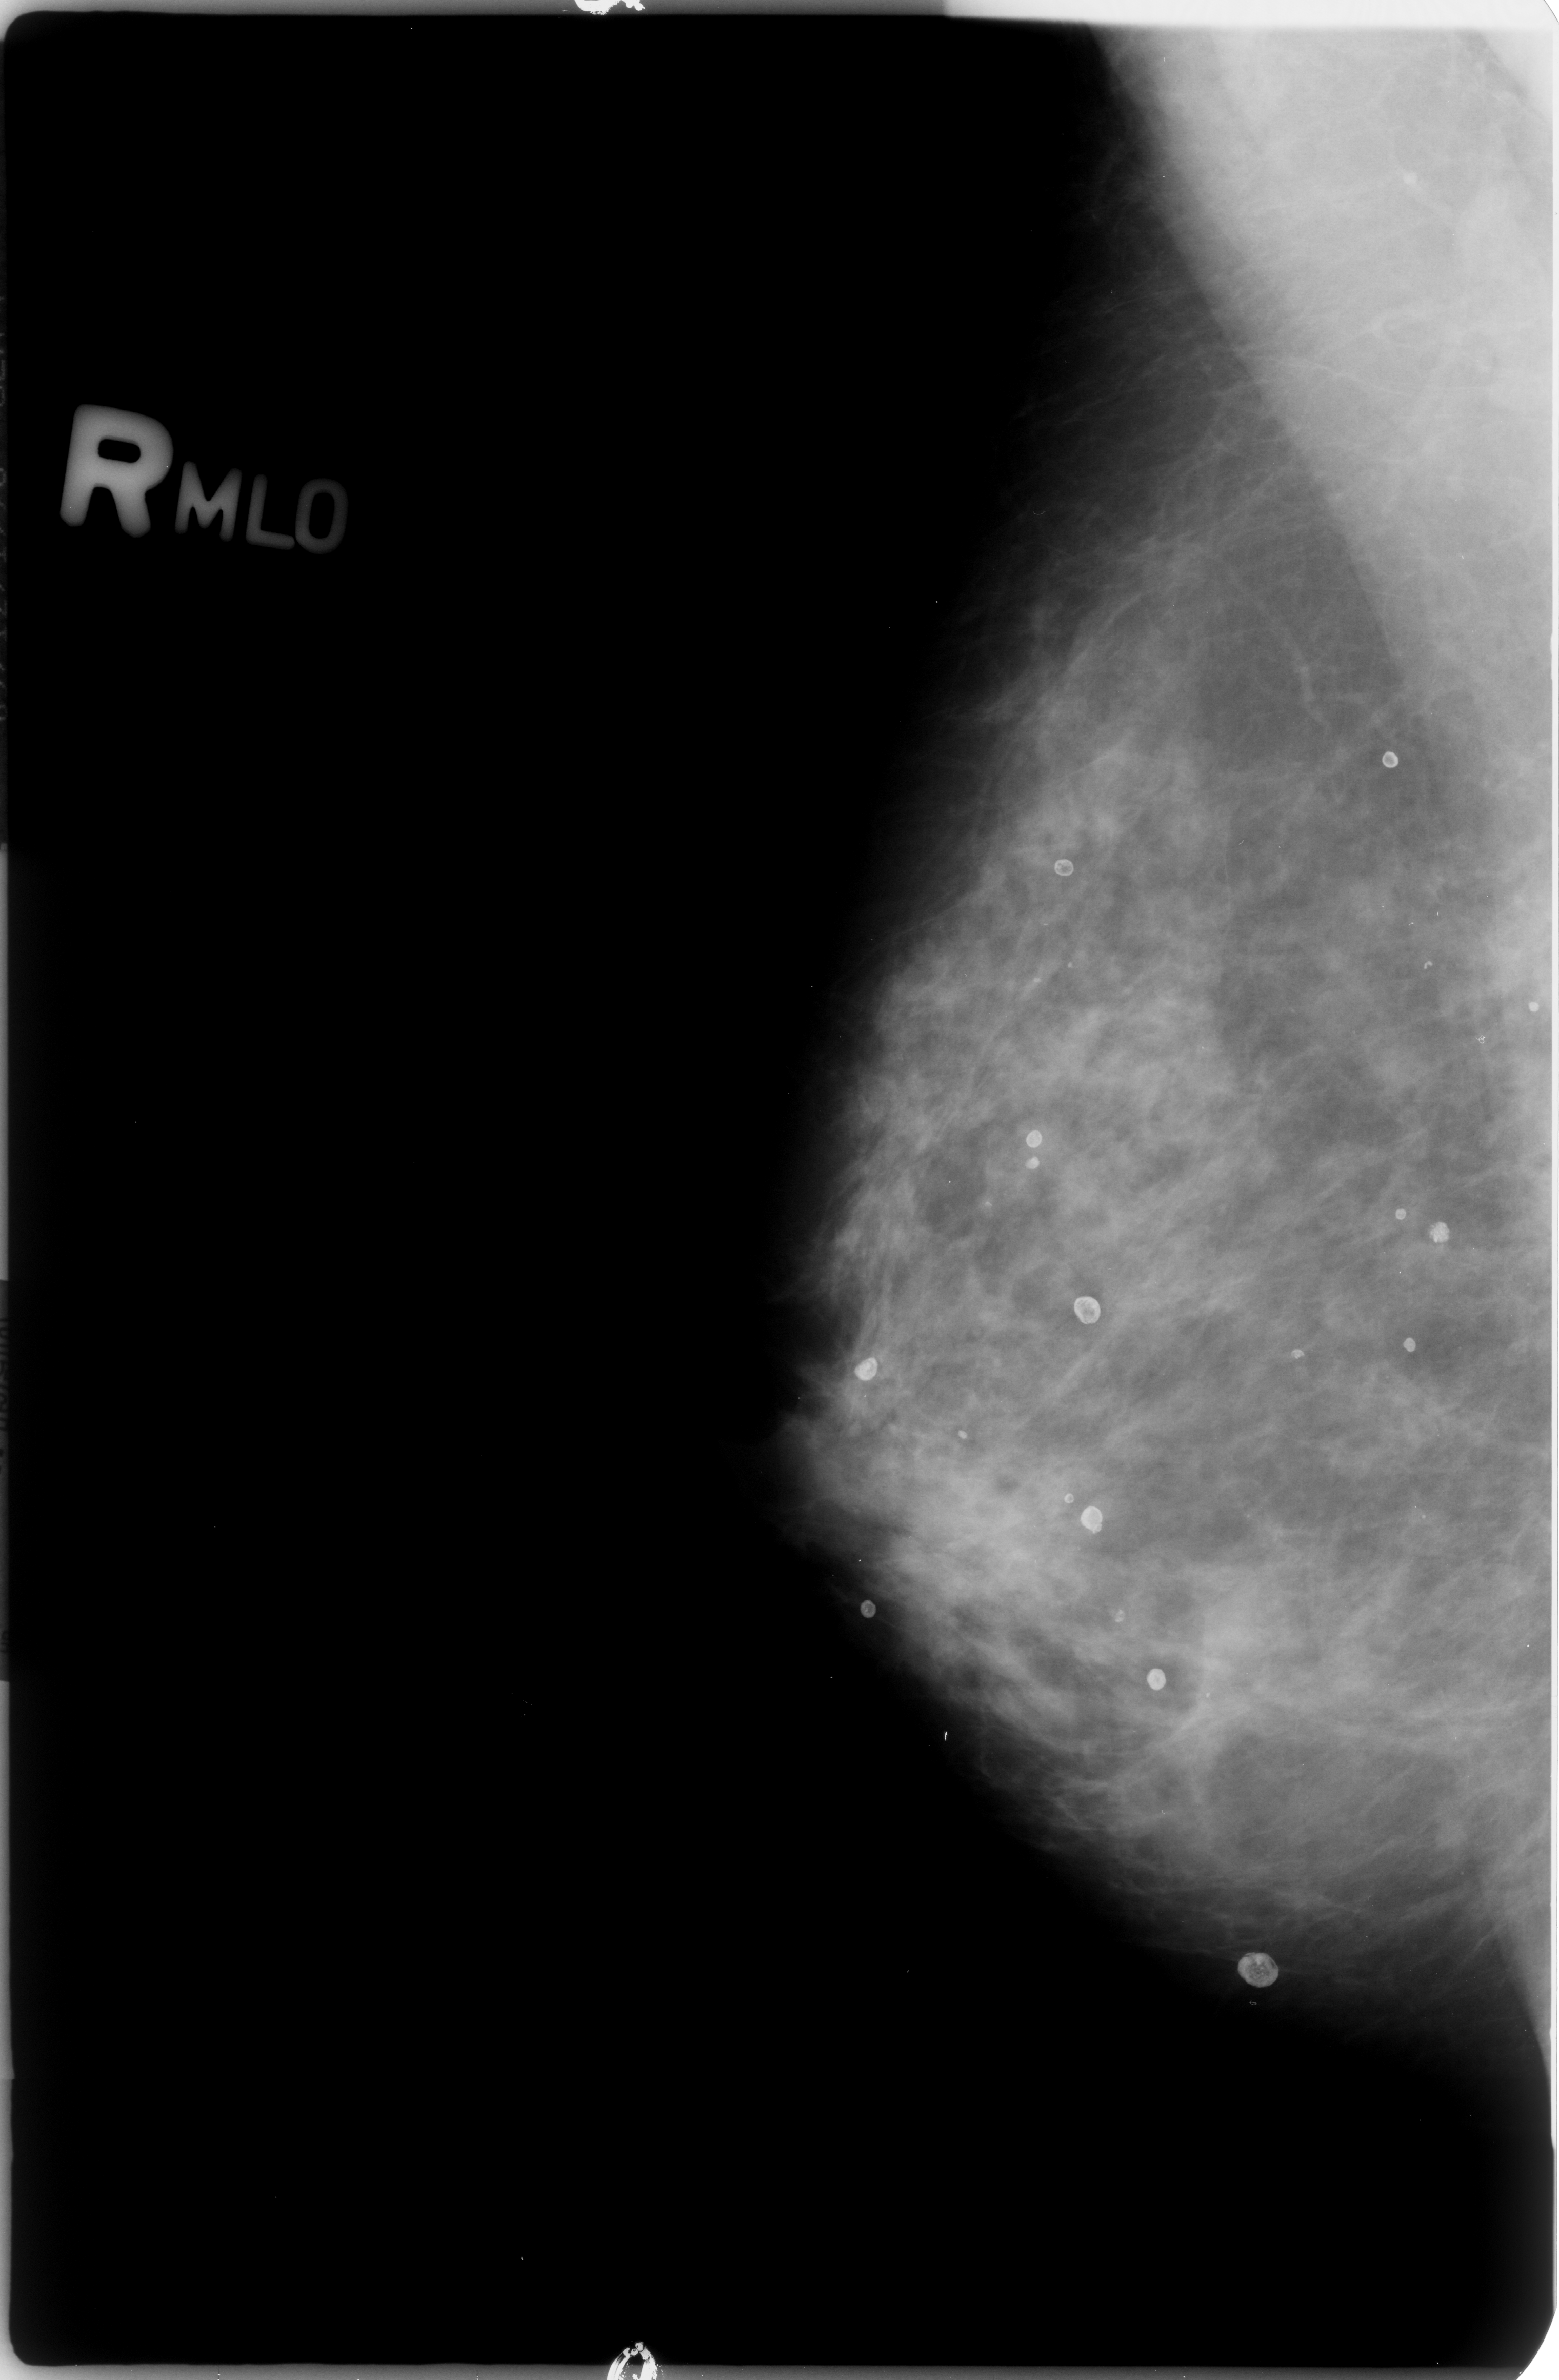
Scanned film-screen mammogram; right breast; mediolateral oblique (MLO) view; 1559 × 2380 image matrix.
Marked abnormalities (boxes around the expert regions of interest):
- Finding 1 of 7: calcifications, morphology round and regular / eggshell; BI-RADS assessment category 2; subtlety rating 3 on a 1 (subtle) to 5 (obvious) scale; benign; no additional work-up was recommended (outcome (as recorded, no biopsy): benign without callback): bounding box (x1, y1, x2, y2) in pixels: (849, 1345, 912, 1404)
- Finding 2 of 7: calcifications, morphology round and regular / eggshell; BI-RADS assessment category 2; subtlety rating 3 on a 1 (subtle) to 5 (obvious) scale; outcome (as recorded, no biopsy): benign without callback (not worked up further): (1017, 1103, 1076, 1183)
- Finding 3 of 7: calcifications, morphology round and regular / eggshell; BI-RADS assessment category 2; subtlety rating 3 on a 1 (subtle) to 5 (obvious) scale; outcome (as recorded, no biopsy): benign without callback (not worked up further): (1050, 1481, 1121, 1564)
- Finding 4 of 7: calcifications, morphology round and regular / eggshell; BI-RADS assessment category 2; outcome (as recorded, no biopsy): benign without callback (not worked up further): (1058, 1259, 1142, 1335)
- Finding 5 of 7: calcifications, morphology round and regular / eggshell; BI-RADS assessment category 2; subtlety rating 3 on a 1 (subtle) to 5 (obvious) scale; benign; no additional work-up was recommended (outcome (as recorded, no biopsy): benign without callback): (1120, 1645, 1195, 1712)
- Finding 6 of 7: calcifications, morphology round and regular / eggshell; BI-RADS assessment category 2; outcome (as recorded, no biopsy): benign without callback (not worked up further): (1222, 1916, 1314, 2012)
- Finding 7 of 7: calcifications, morphology round and regular / eggshell; BI-RADS assessment category 2; outcome (as recorded, no biopsy): benign without callback (not worked up further): (1407, 1206, 1466, 1265)